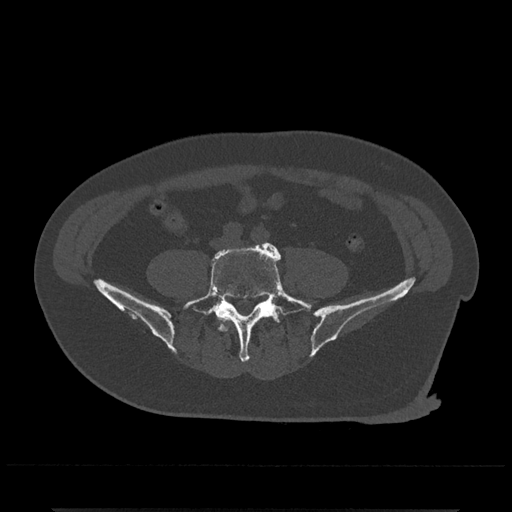
CT including the spine, one axial slice. Slice 91 of 797 in the series (ordered by position). Reconstruction kernel Br40s/3. 120 kVp. Bone window (W 1800 / L 400 HU). 0.5 mm slice thickness. 512 × 512 image matrix, field of view 393 × 393 mm. Male patient, age 67 years. Case-level facts recorded for this patient, not image findings: primary cancer: prostate.
Structures marked on this image (semi-automatic segmentation, software-assisted and operator-edited):
- L4 vertebra: box from (x=221, y=326) to (x=228, y=331) px
- L5 vertebra: (x=183, y=242)–(x=312, y=363)